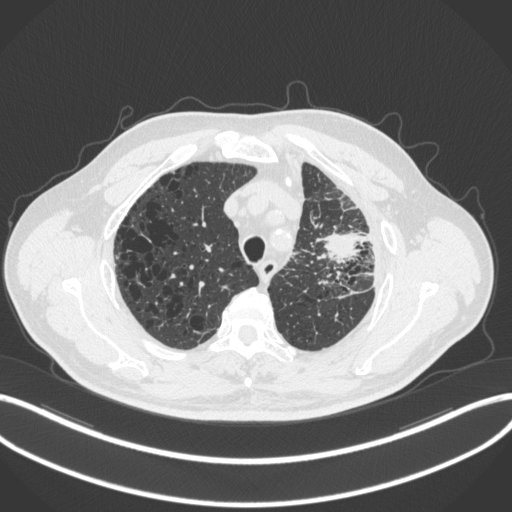
Chest CT, one axial slice; position 245 of 286 along the scan axis; reconstruction kernel B31f; lung window (W 1500 / L -600 HU); 1 mm slice thickness; 512 × 512 image matrix, field of view 400 × 400 mm. Patient: male, 68 years. From the clinical record (not read from this slice): clinical TNM (as recorded): T3 N3 M1.
Annotated regions visible in this slice (rectangle marked by the reading radiologist):
- lung tumour (recorded histology: adenocarcinoma): bounding box (x1, y1, x2, y2) in pixels: (314, 225, 363, 267)